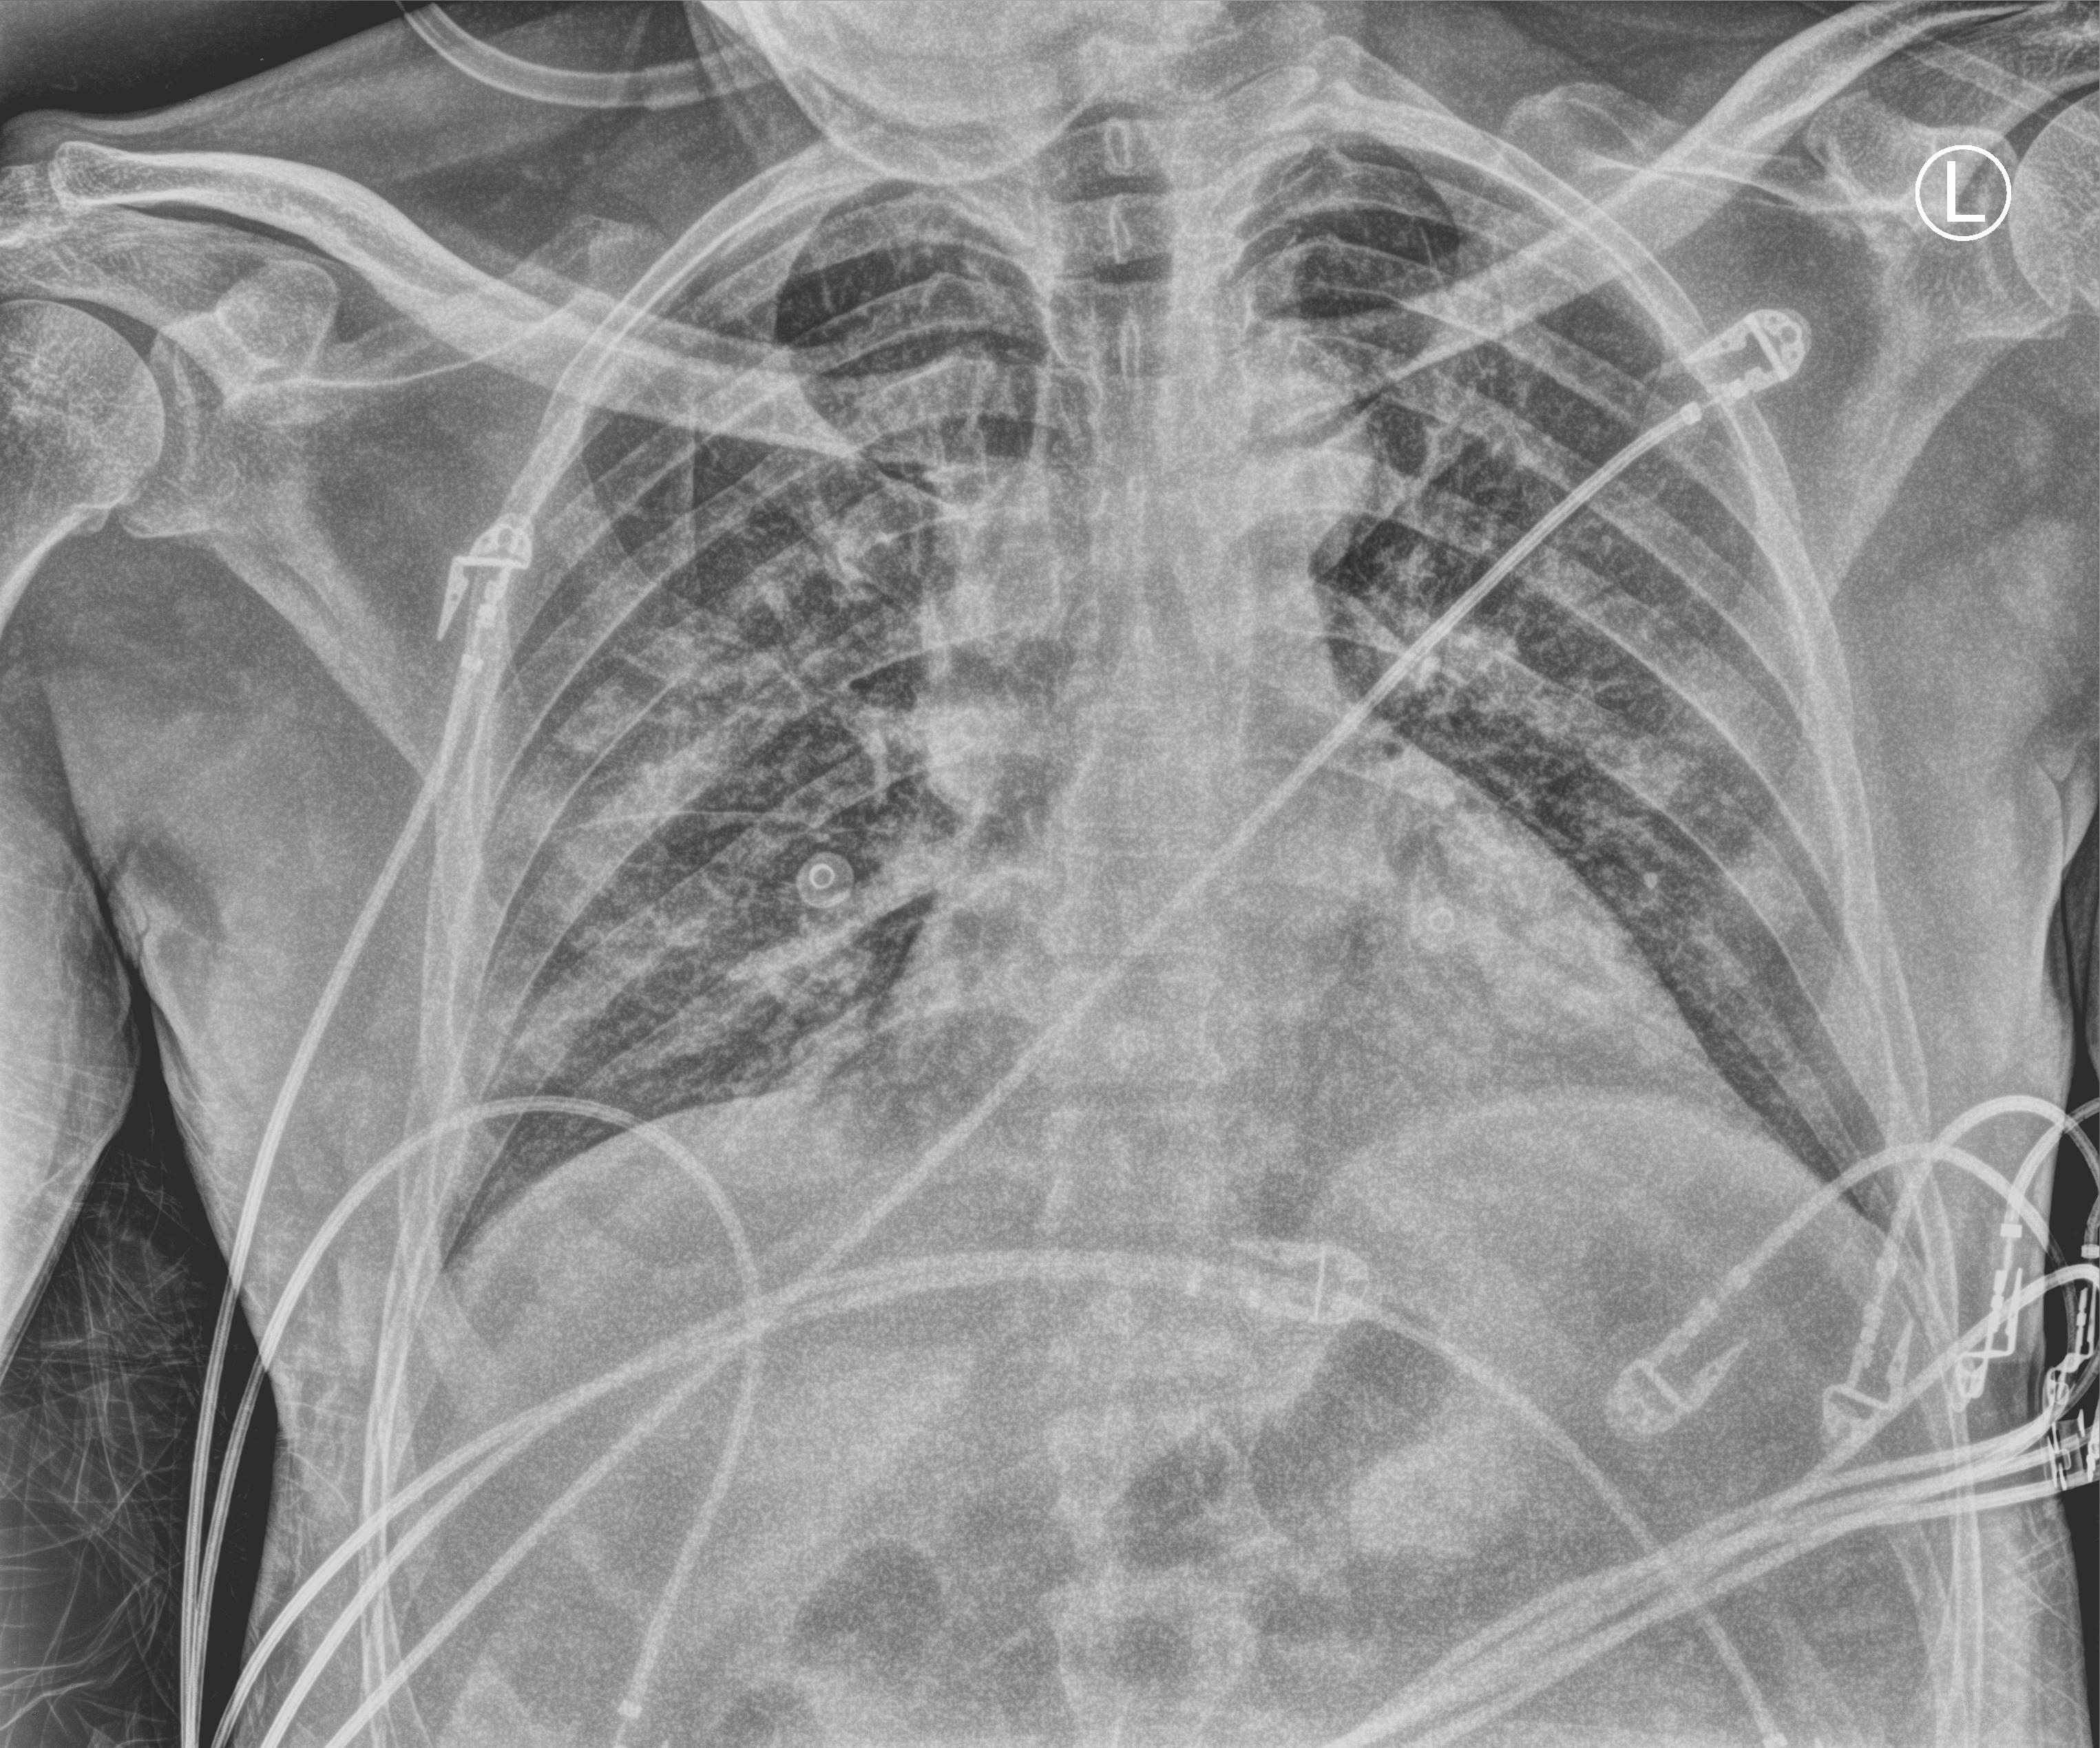
Bedside chest radiograph (computed radiography); anteroposterior (AP) projection. Male patient hospitalised with COVID-19, age 18–59 years.
Hospital-stay facts (about this admission, not read from this image; timing relative to this image not recorded):
- admitted to intensive care during this hospital stay: yes
- mechanically ventilated during this hospital stay: yes